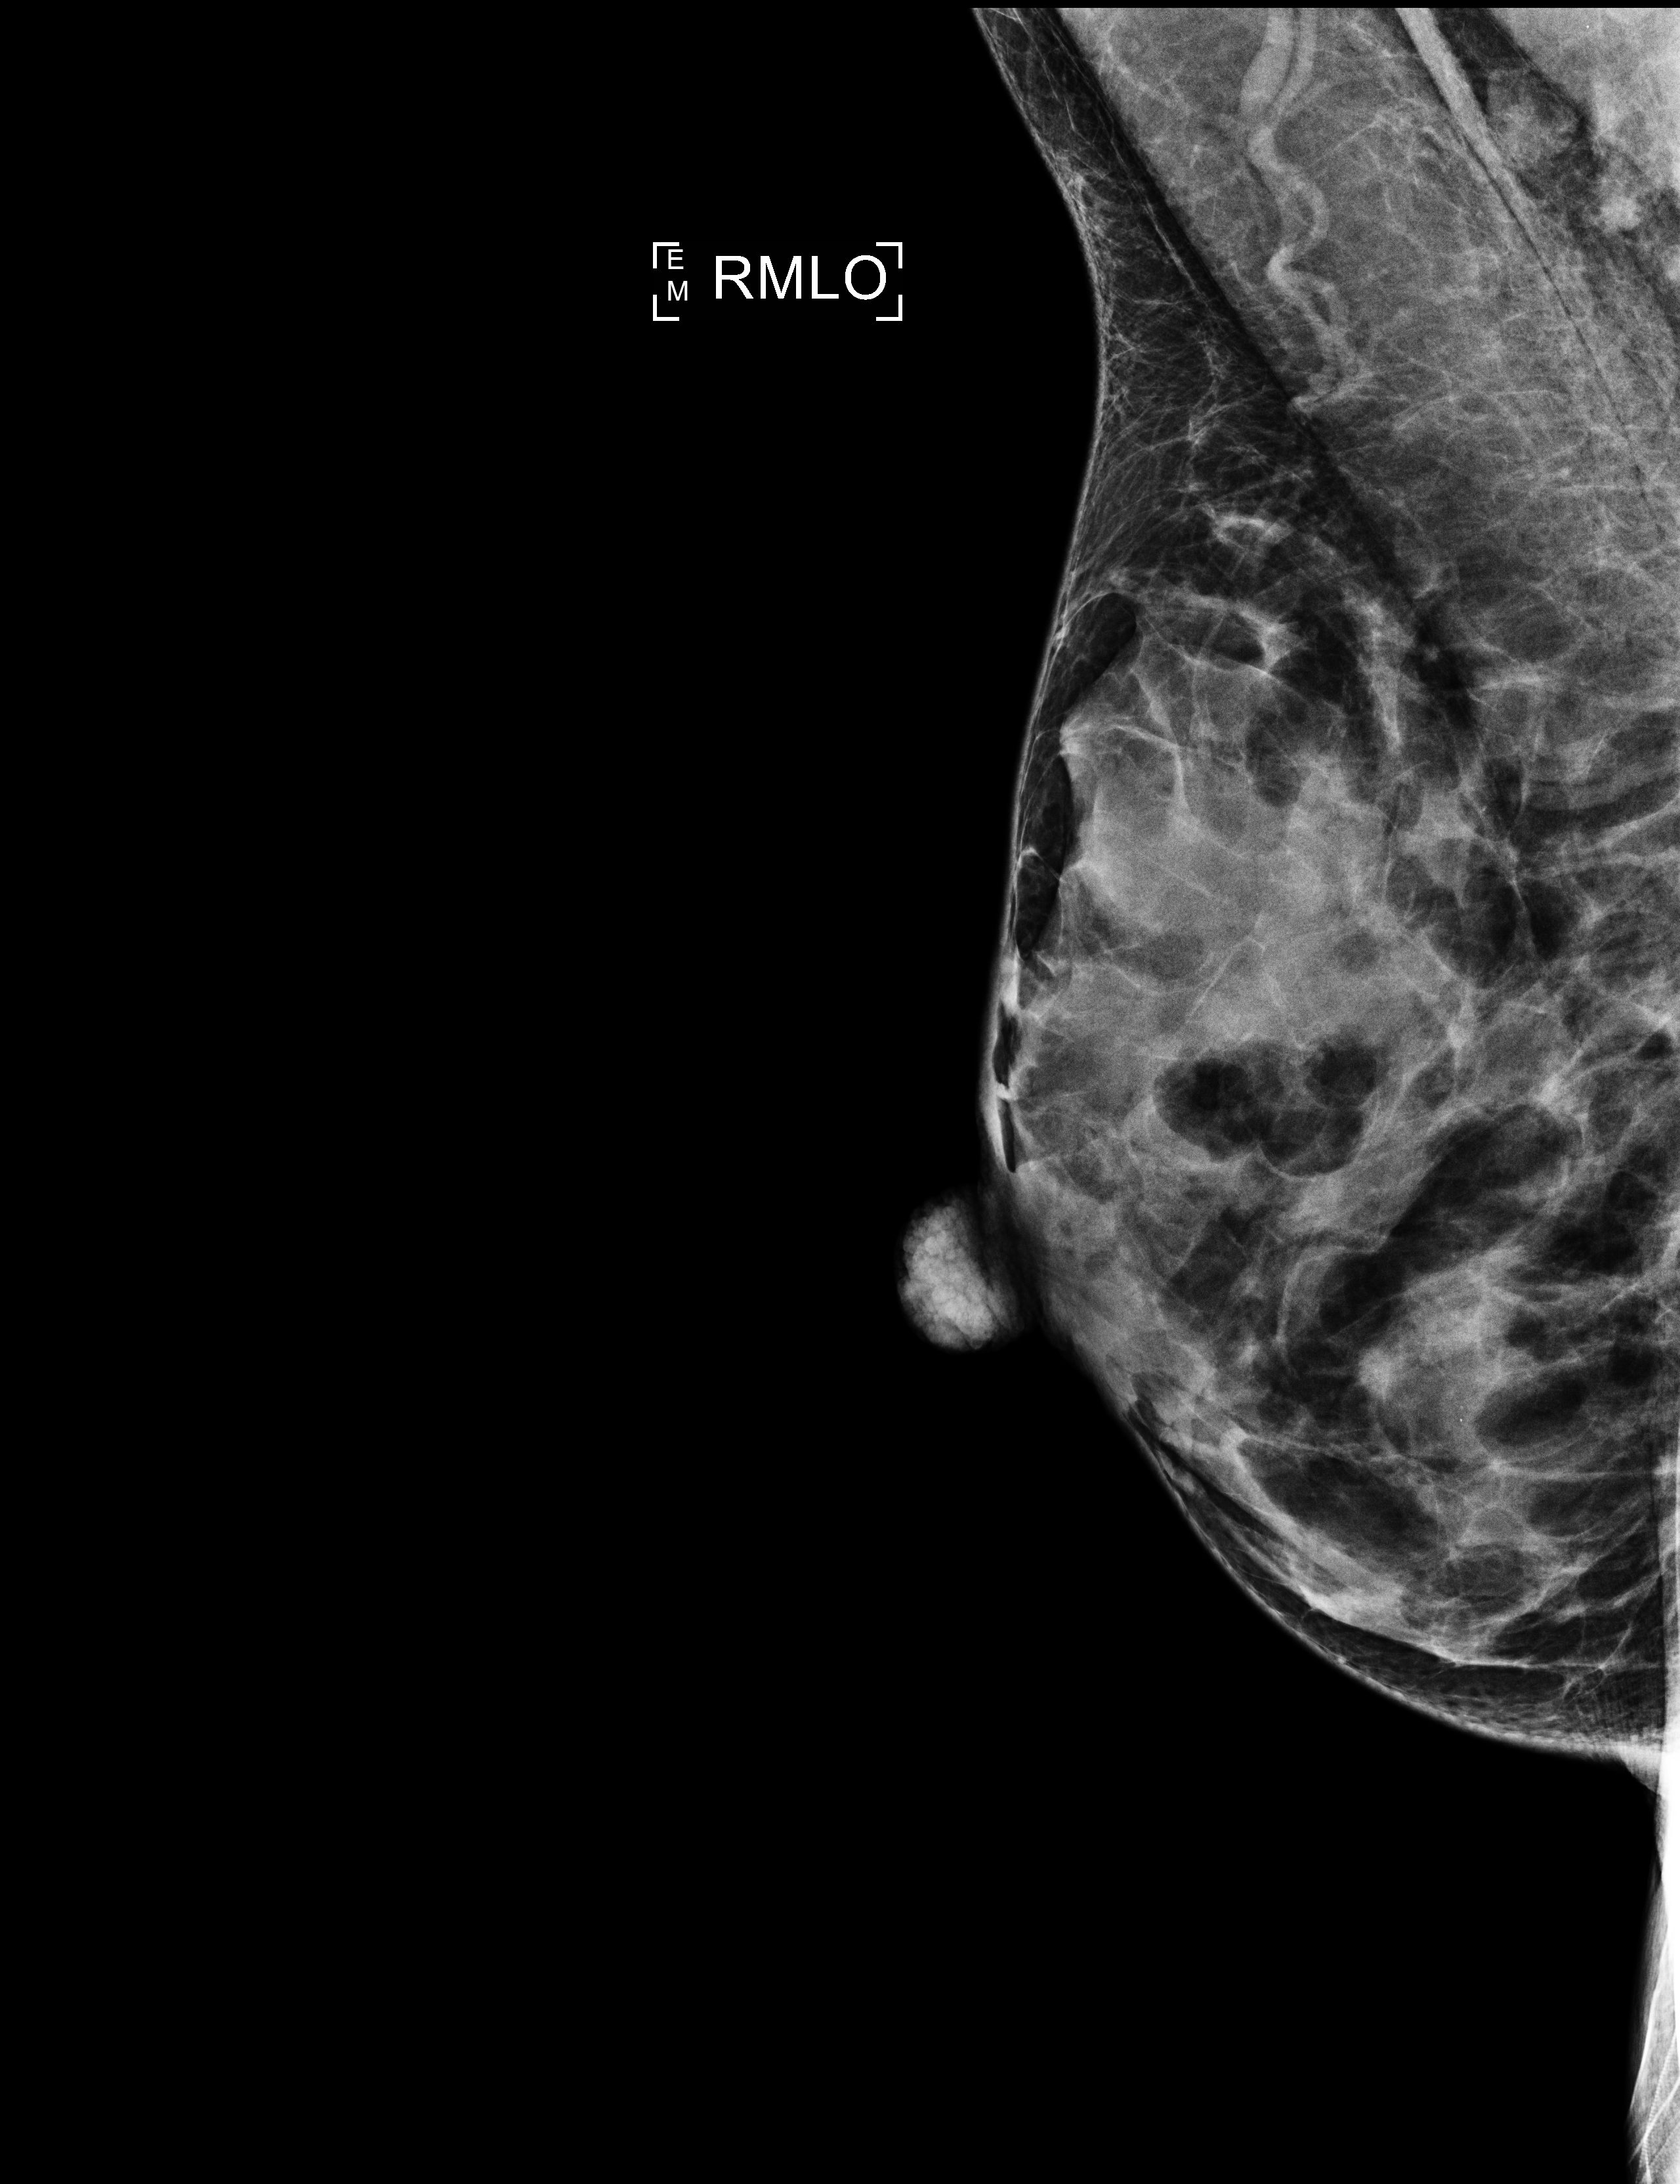
Full-field digital mammogram (FFDM); right breast; MLO view; screening examination; compressed breast thickness 39 mm; system: Selenia Dimensions. Patient: female, 42 years.
- BI-RADS breast density category at the screening exam (both breasts, scale 1–4): 4
- final BI-RADS assessment for this screening round (tomosynthesis exam, both breasts): category 2
- recall: recalled for additional imaging after this screen